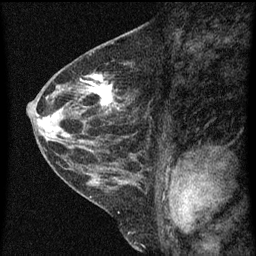
Breast MRI (dynamic contrast-enhanced), one sagittal slice. Position 27 of 60 along the scan axis. Dynamic contrast-enhanced series, image 2 of 3 at this slice position (ordered by acquisition). 1.5 T. TE 4.2 ms, TR 8 ms. 2 mm slice thickness. 256 × 256 image matrix, field of view 180 × 180 mm. Patient: female, 48 years.
Annotated regions visible in this slice (semi-automatic segmentation, software-assisted and operator-edited):
- analysis volume of interest (the breast-tissue region the enhancement analysis was run in; not a lesion): bounding box <82,72,126,125> (left, top, right, bottom; pixels)
- tumour enhancement mask (voxels above the 70 % enhancement threshold inside the analysis volume of interest): <87,74,117,105>